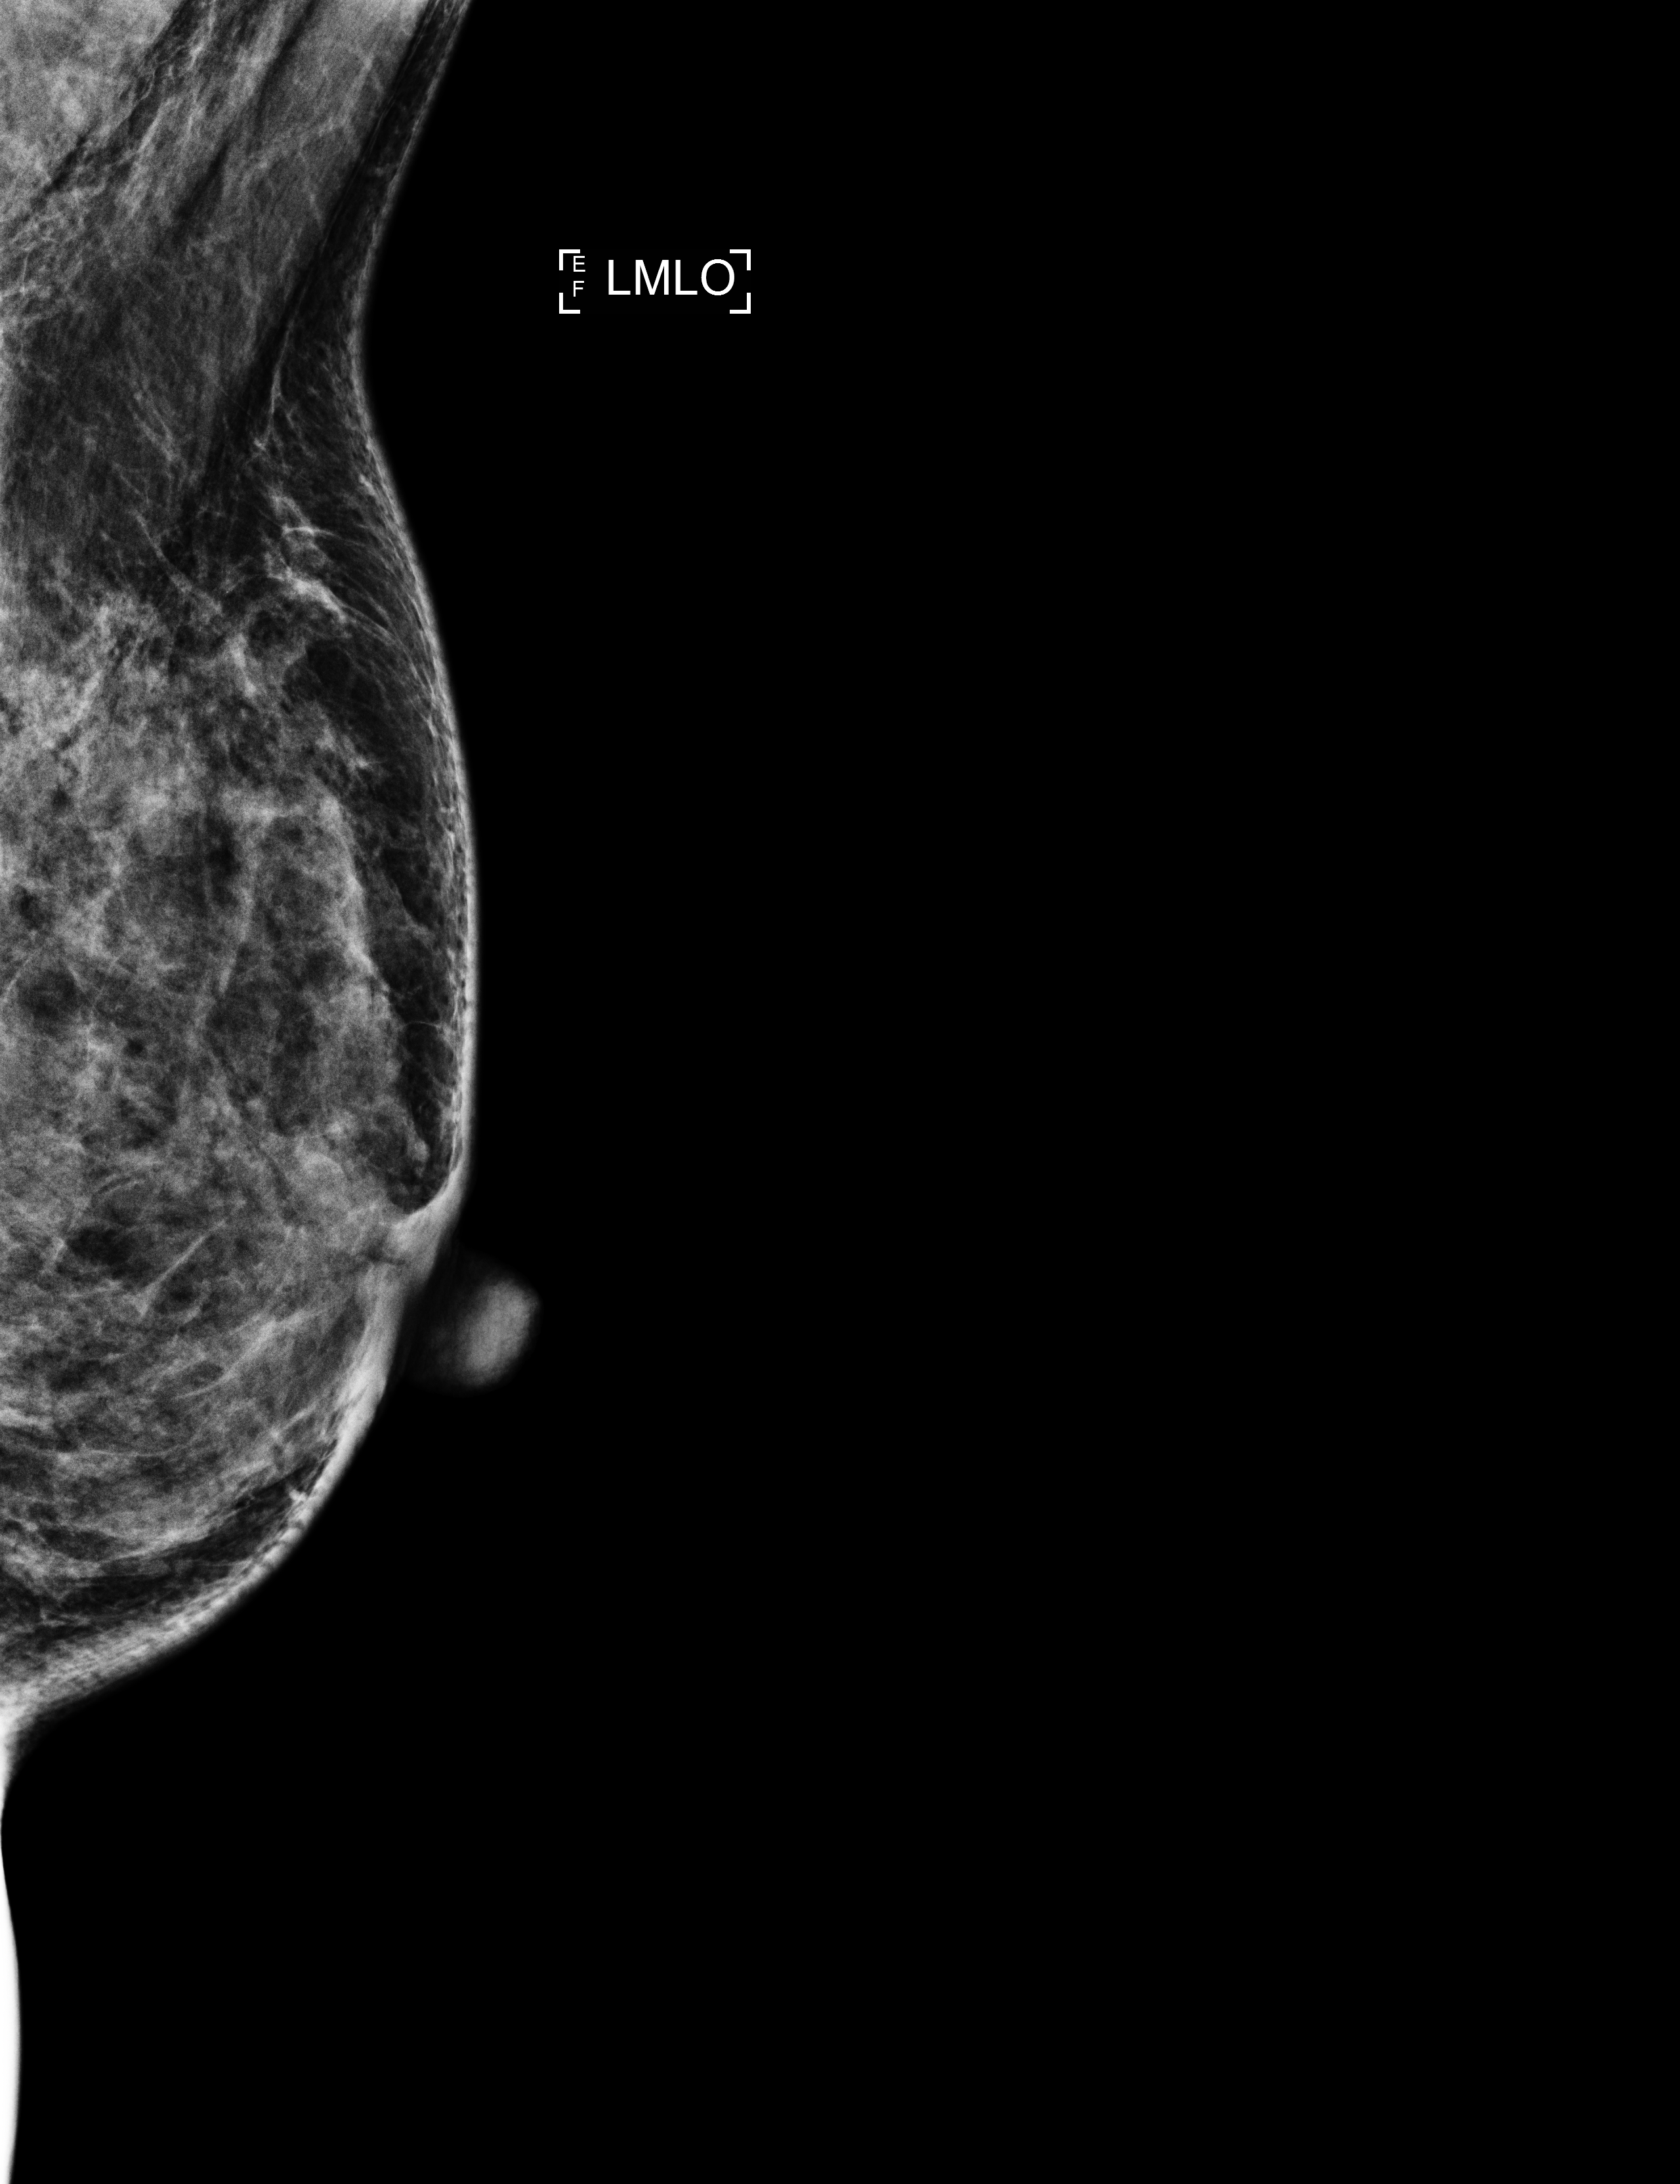
Annual screening mammography examination, compressed breast thickness 35 mm. Patient aged 59 years (female).
Image type: full-field digital mammogram. Breast: left. Projection: medio-lateral oblique projection.